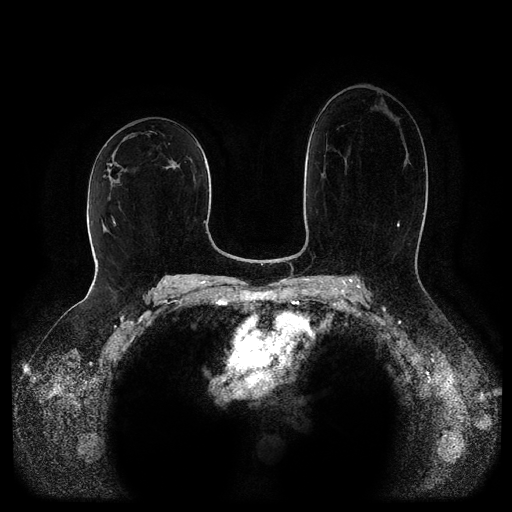
Breast MRI (dynamic contrast-enhanced, multi-phase), one axial slice; position 55 of 116 along the scan axis; dynamic contrast-enhanced series, time point 2 of 5 at this slice position (early post-contrast); 1.5 T; TE 2.6 ms, TR 5.2 ms; 2 mm slice thickness; 512 × 512 image matrix. Female patient, age 52 years.
Structures marked on this image (semi-automatically segmented with operator editing):
- breast lesion (labelled 'tumour' in the annotation; benign lesions carry a separate 'benign' label): bounding box (x1, y1, x2, y2) in pixels: (163, 160, 180, 169)